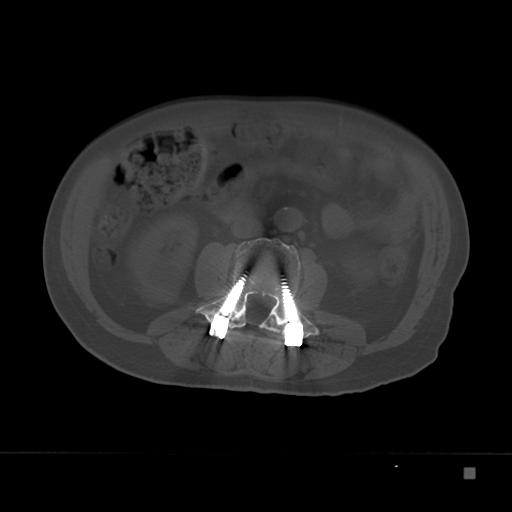
CT including the spine, one axial slice. Position 71 of 332 along the scan axis. Reconstruction kernel Br40s. 120 kVp. Bone window (W 1800 / L 400 HU). 1.5 mm slice thickness. 512 × 512 image matrix, field of view 389 × 389 mm. Patient: male, 72 years. Case-level facts recorded for this patient, not image findings: primary cancer: skeletal.
Annotated regions visible in this slice (semi-automatically segmented with operator editing):
- L3 vertebra: box from (x=195, y=237) to (x=322, y=338) px